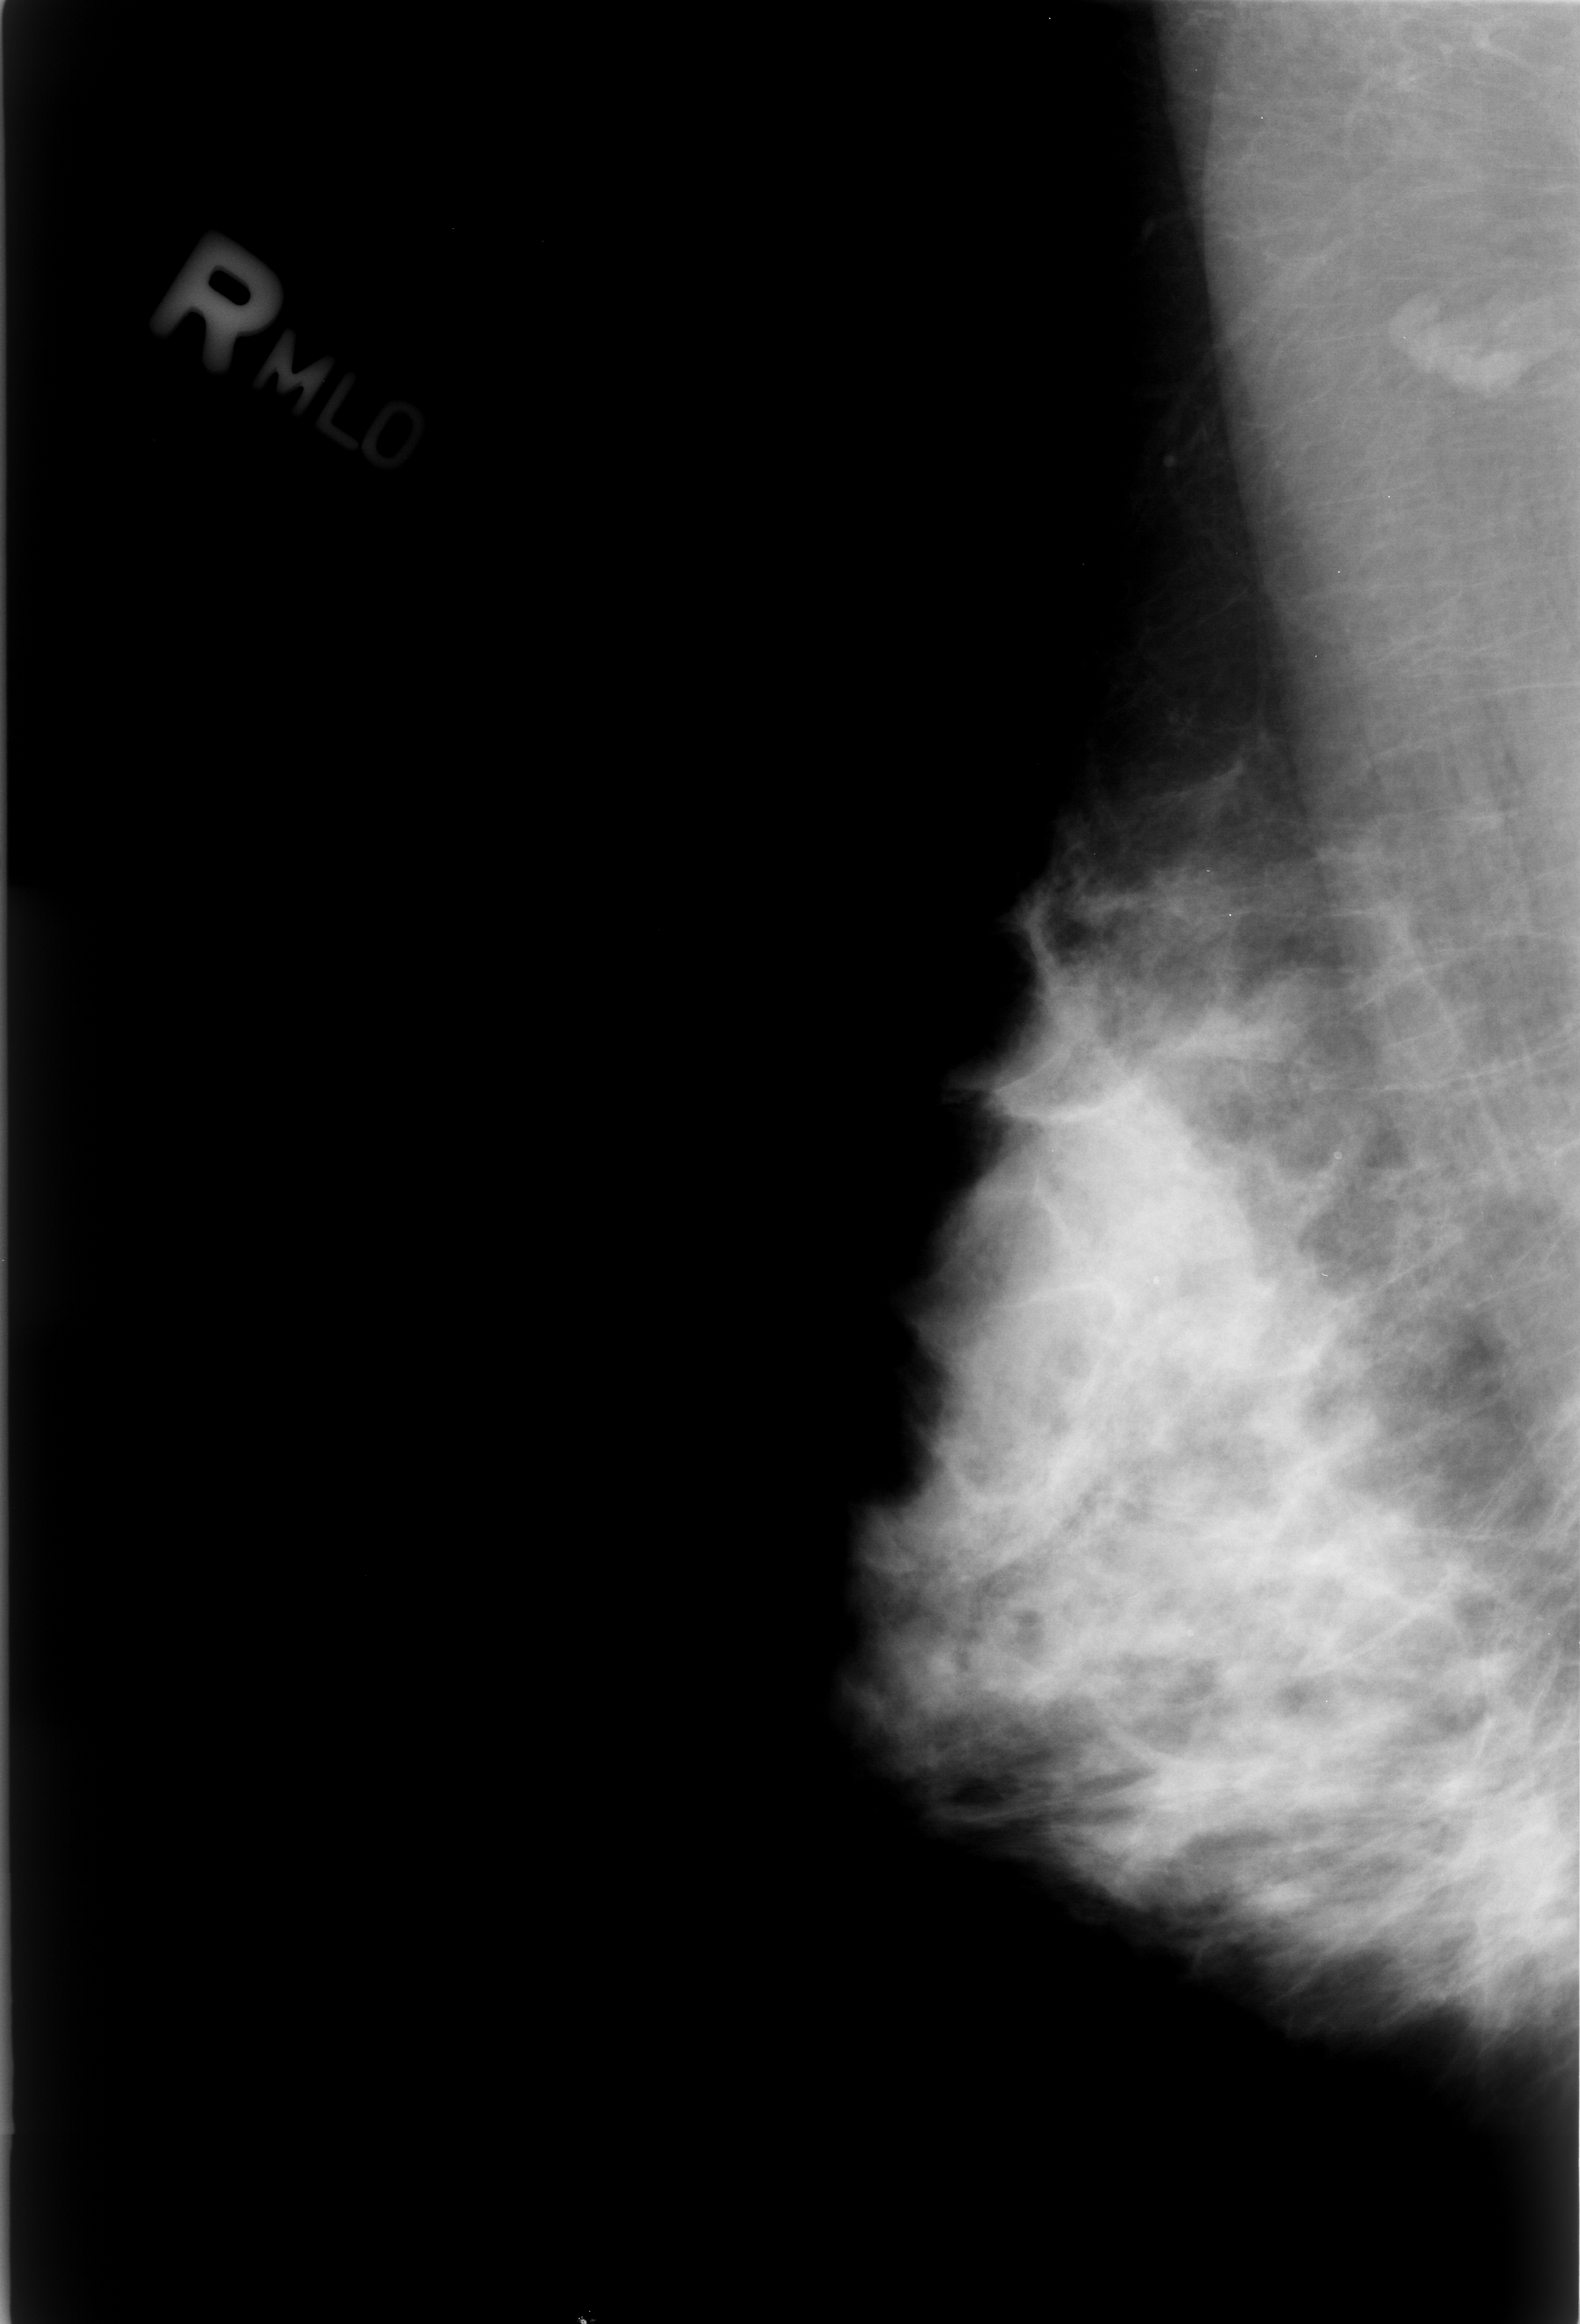
Digitized screen-film mammogram; right breast; MLO view.
- Abnormality record for this image: Finding 1 of 3: calcifications, morphology lucent center; BI-RADS assessment category 2; subtlety rating 4 on a 1 (subtle) to 5 (obvious) scale; benign; no additional work-up was recommended (benign without callback).
- Finding 2 of 3: calcifications, morphology lucent center; BI-RADS assessment category 2; benign; no additional work-up was recommended (benign without callback).
- Finding 3 of 3: calcifications, morphology lucent center; BI-RADS assessment category 2; benign without callback (not worked up further).